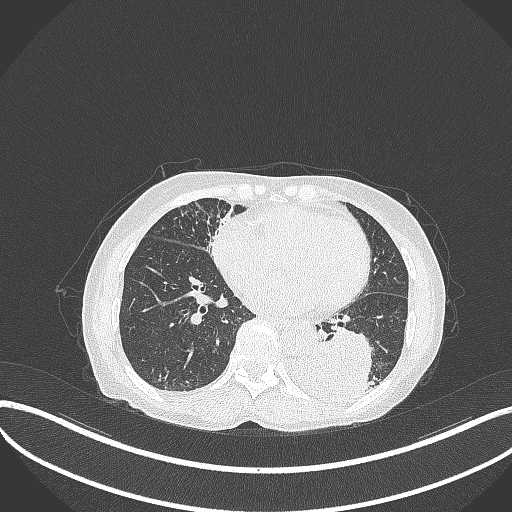
Chest CT, one axial slice. Position 111 of 370 along the scan axis. 120 kVp. Lung window (W 1500 / L -600 HU). 1 mm slice thickness. 512 × 512 image matrix. Female patient, age 78 years. Case-level facts recorded for this patient, not image findings: clinical TNM (as recorded): T3 N0 M1.
Outlined on this slice (rectangle marked by the reading radiologist):
- lung tumour (recorded histology: squamous cell carcinoma): bounding box <283,328,376,407> (left, top, right, bottom; pixels)